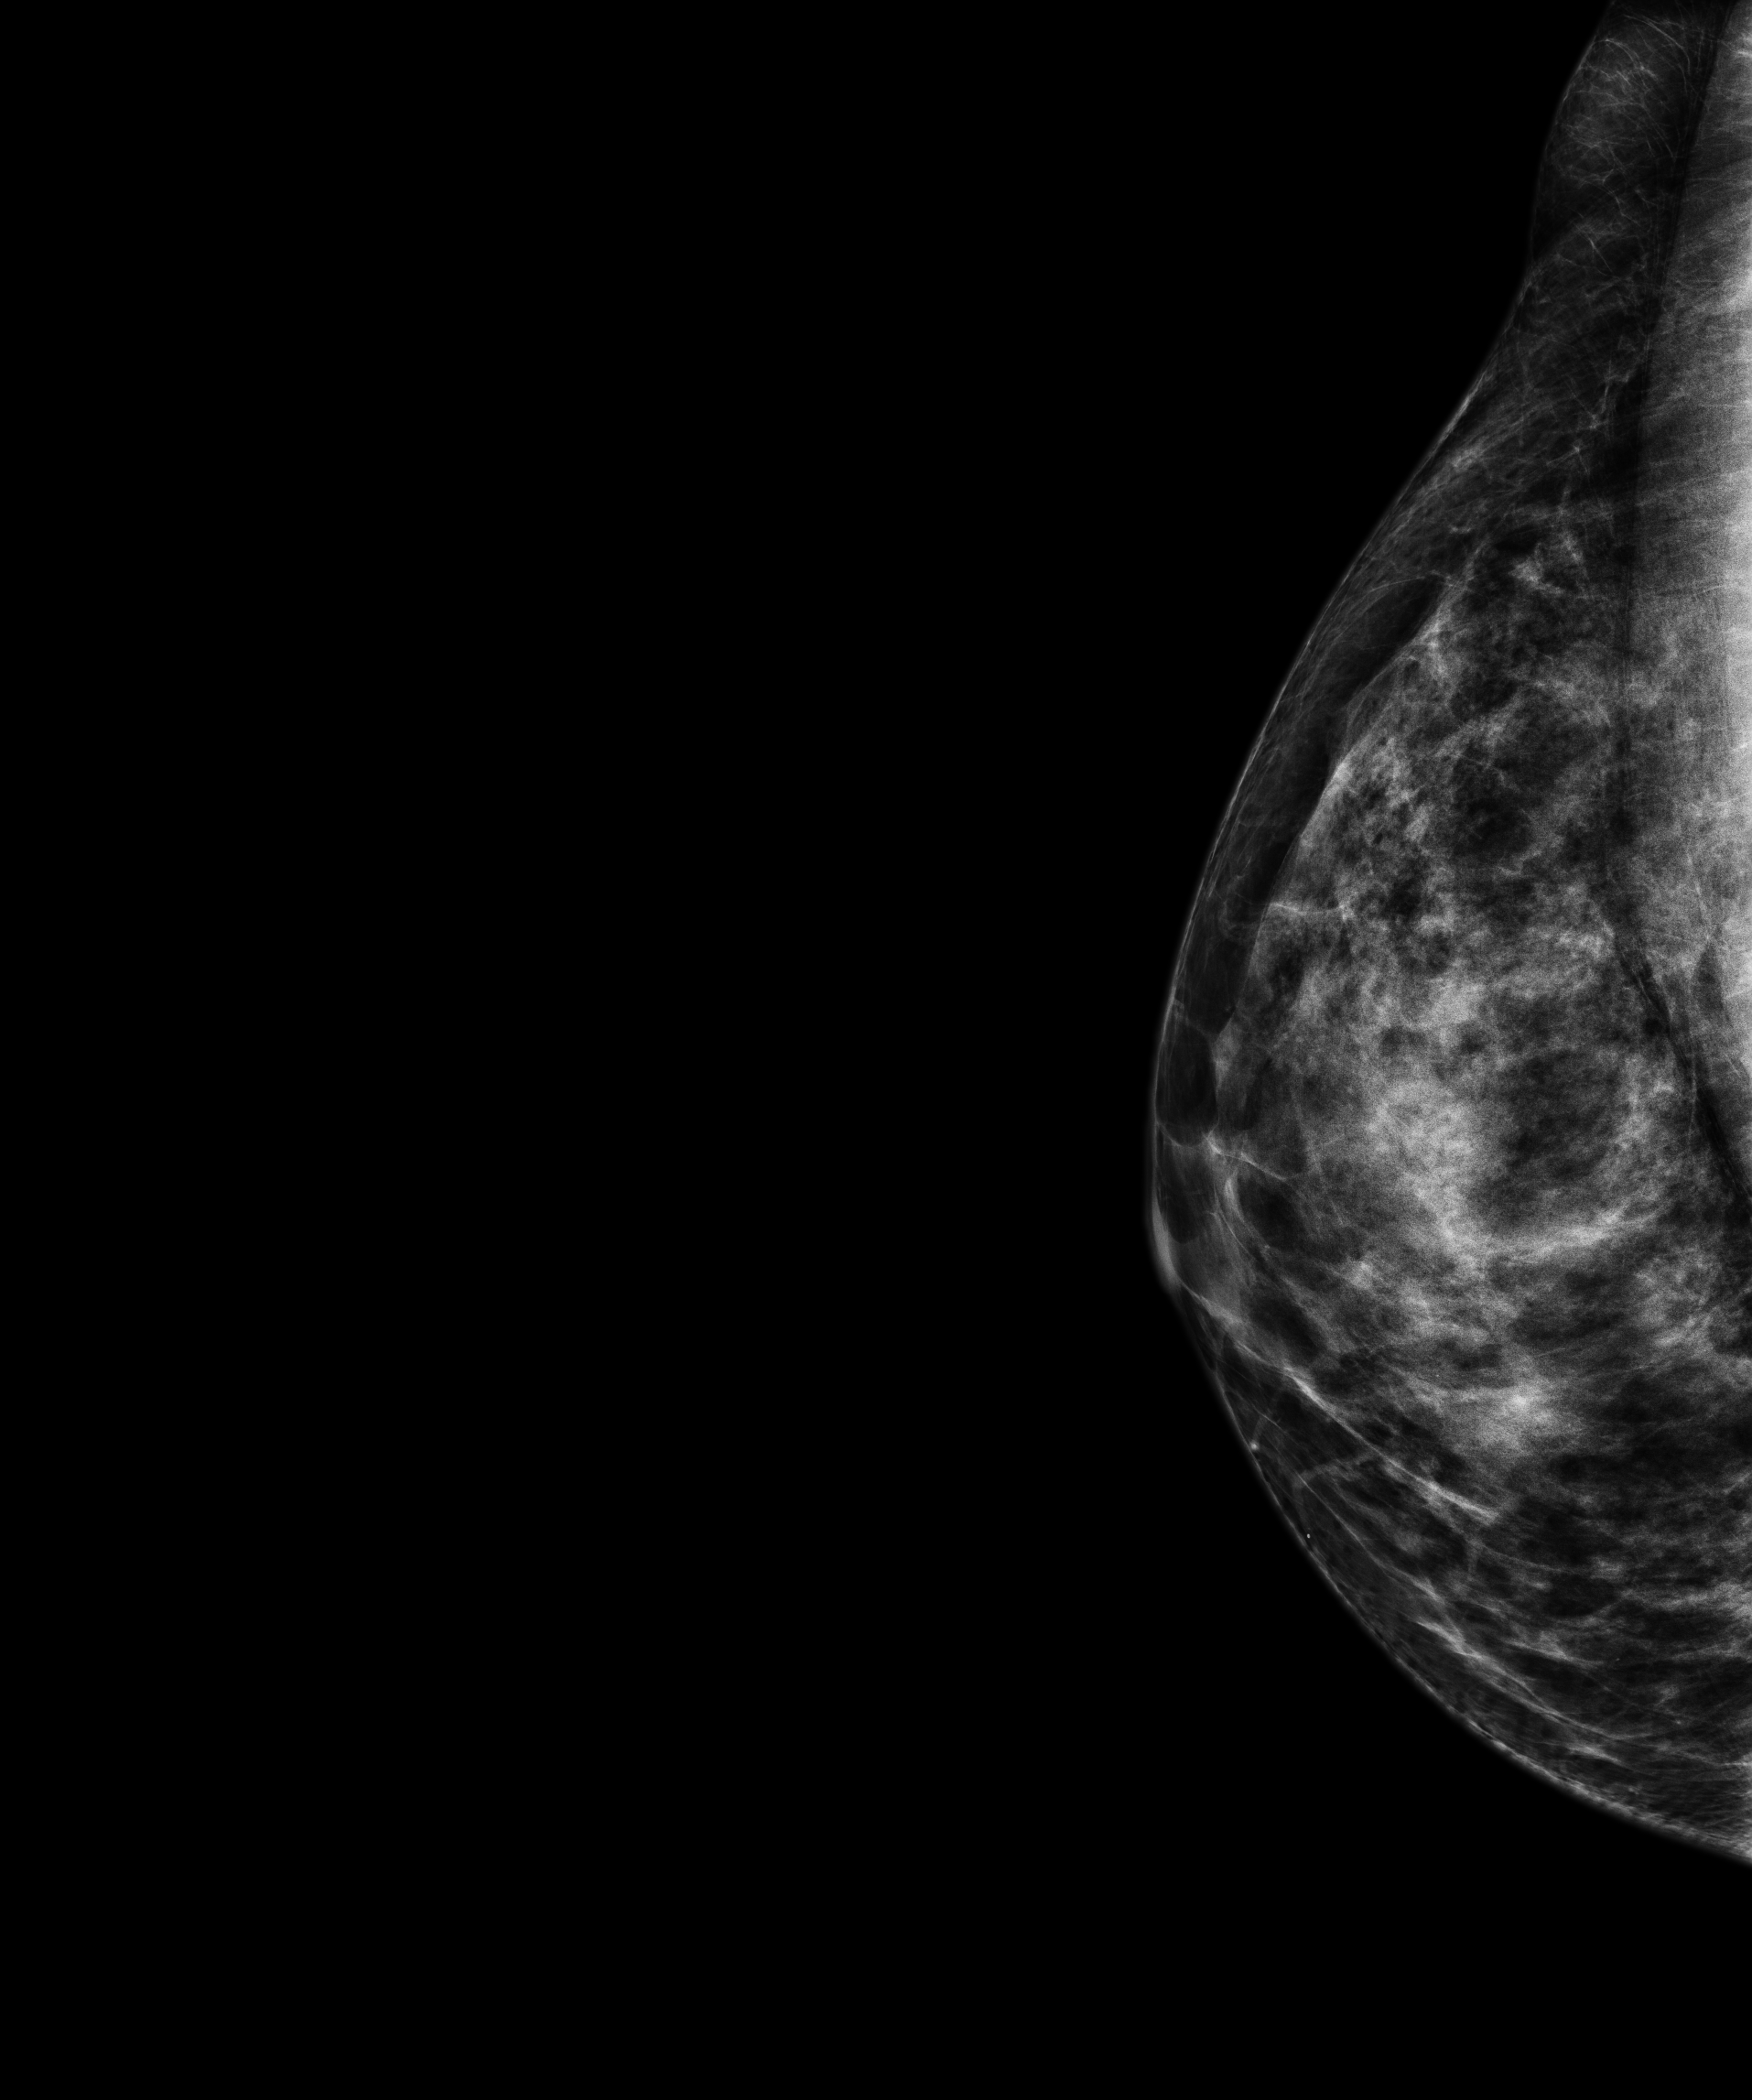
Annual screening mammography examination. Patient aged 44 years (female).
Image type: full-field digital mammogram. Breast: right. Projection: laterally exaggerated craniocaudal (XCCL) view.